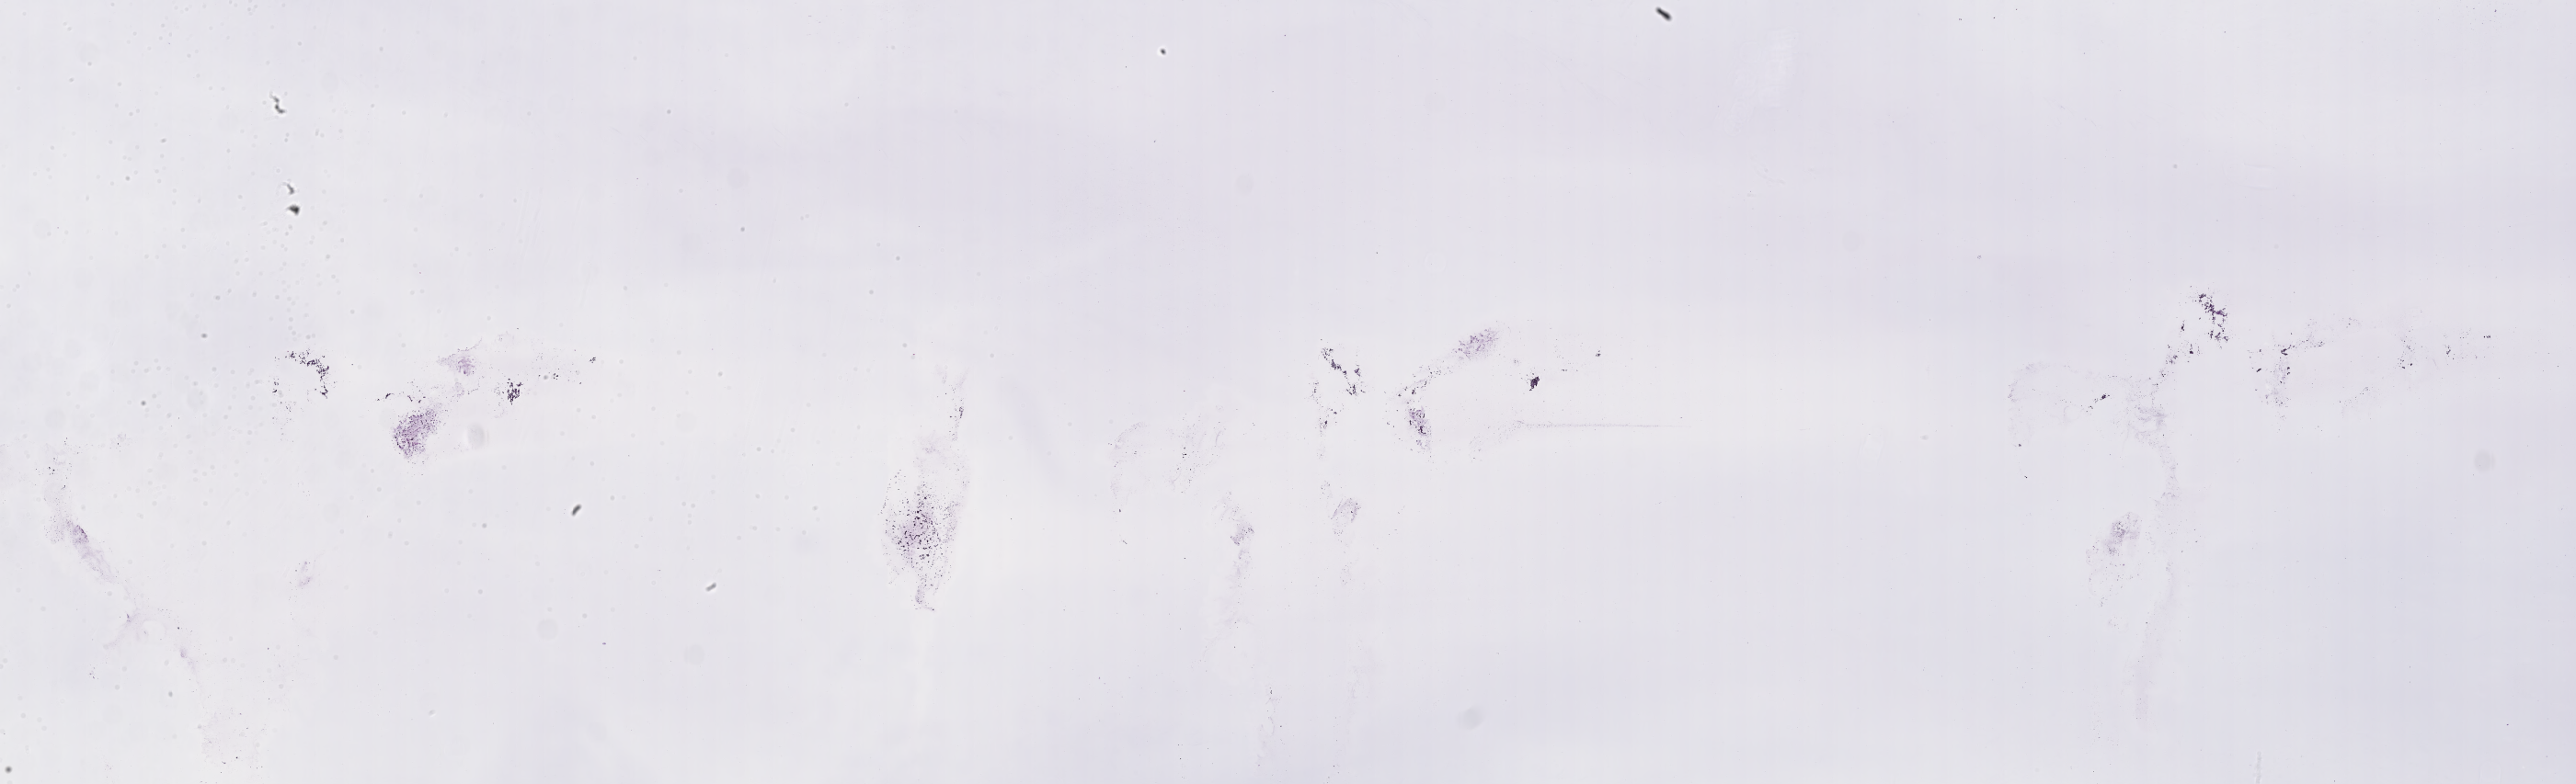
Hematoxylin and eosin (H&E) whole-slide image of tumor tissue from the brain — low-resolution overview of the scanned area, about 45.3 x 13.8 mm; cryosection (OCT / tissue freezing medium). Patient female; age 129 months (10 years 9 months).
Diagnosis: Medulloblastoma, NOS.